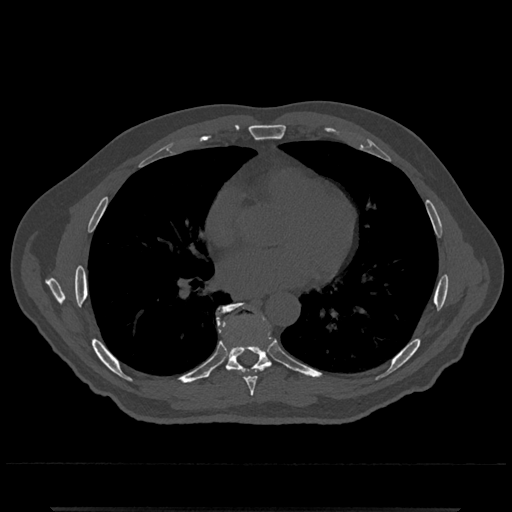
CT including the spine, one axial slice. Position 694 of 797 along the scan axis. Reconstruction kernel Br40s/3. Bone window (W 1800 / L 400 HU). 0.5 mm slice thickness. 512 × 512 image matrix, field of view 393 × 393 mm. Patient: male, 67 years. Case-level facts recorded for this patient, not image findings: primary cancer: prostate.
Annotated regions visible in this slice (semi-automatic segmentation, software-assisted and operator-edited):
- T7 vertebra: bounding box <225,365,271,396> (left, top, right, bottom; pixels)
- T8 vertebra: <216,302,271,373>